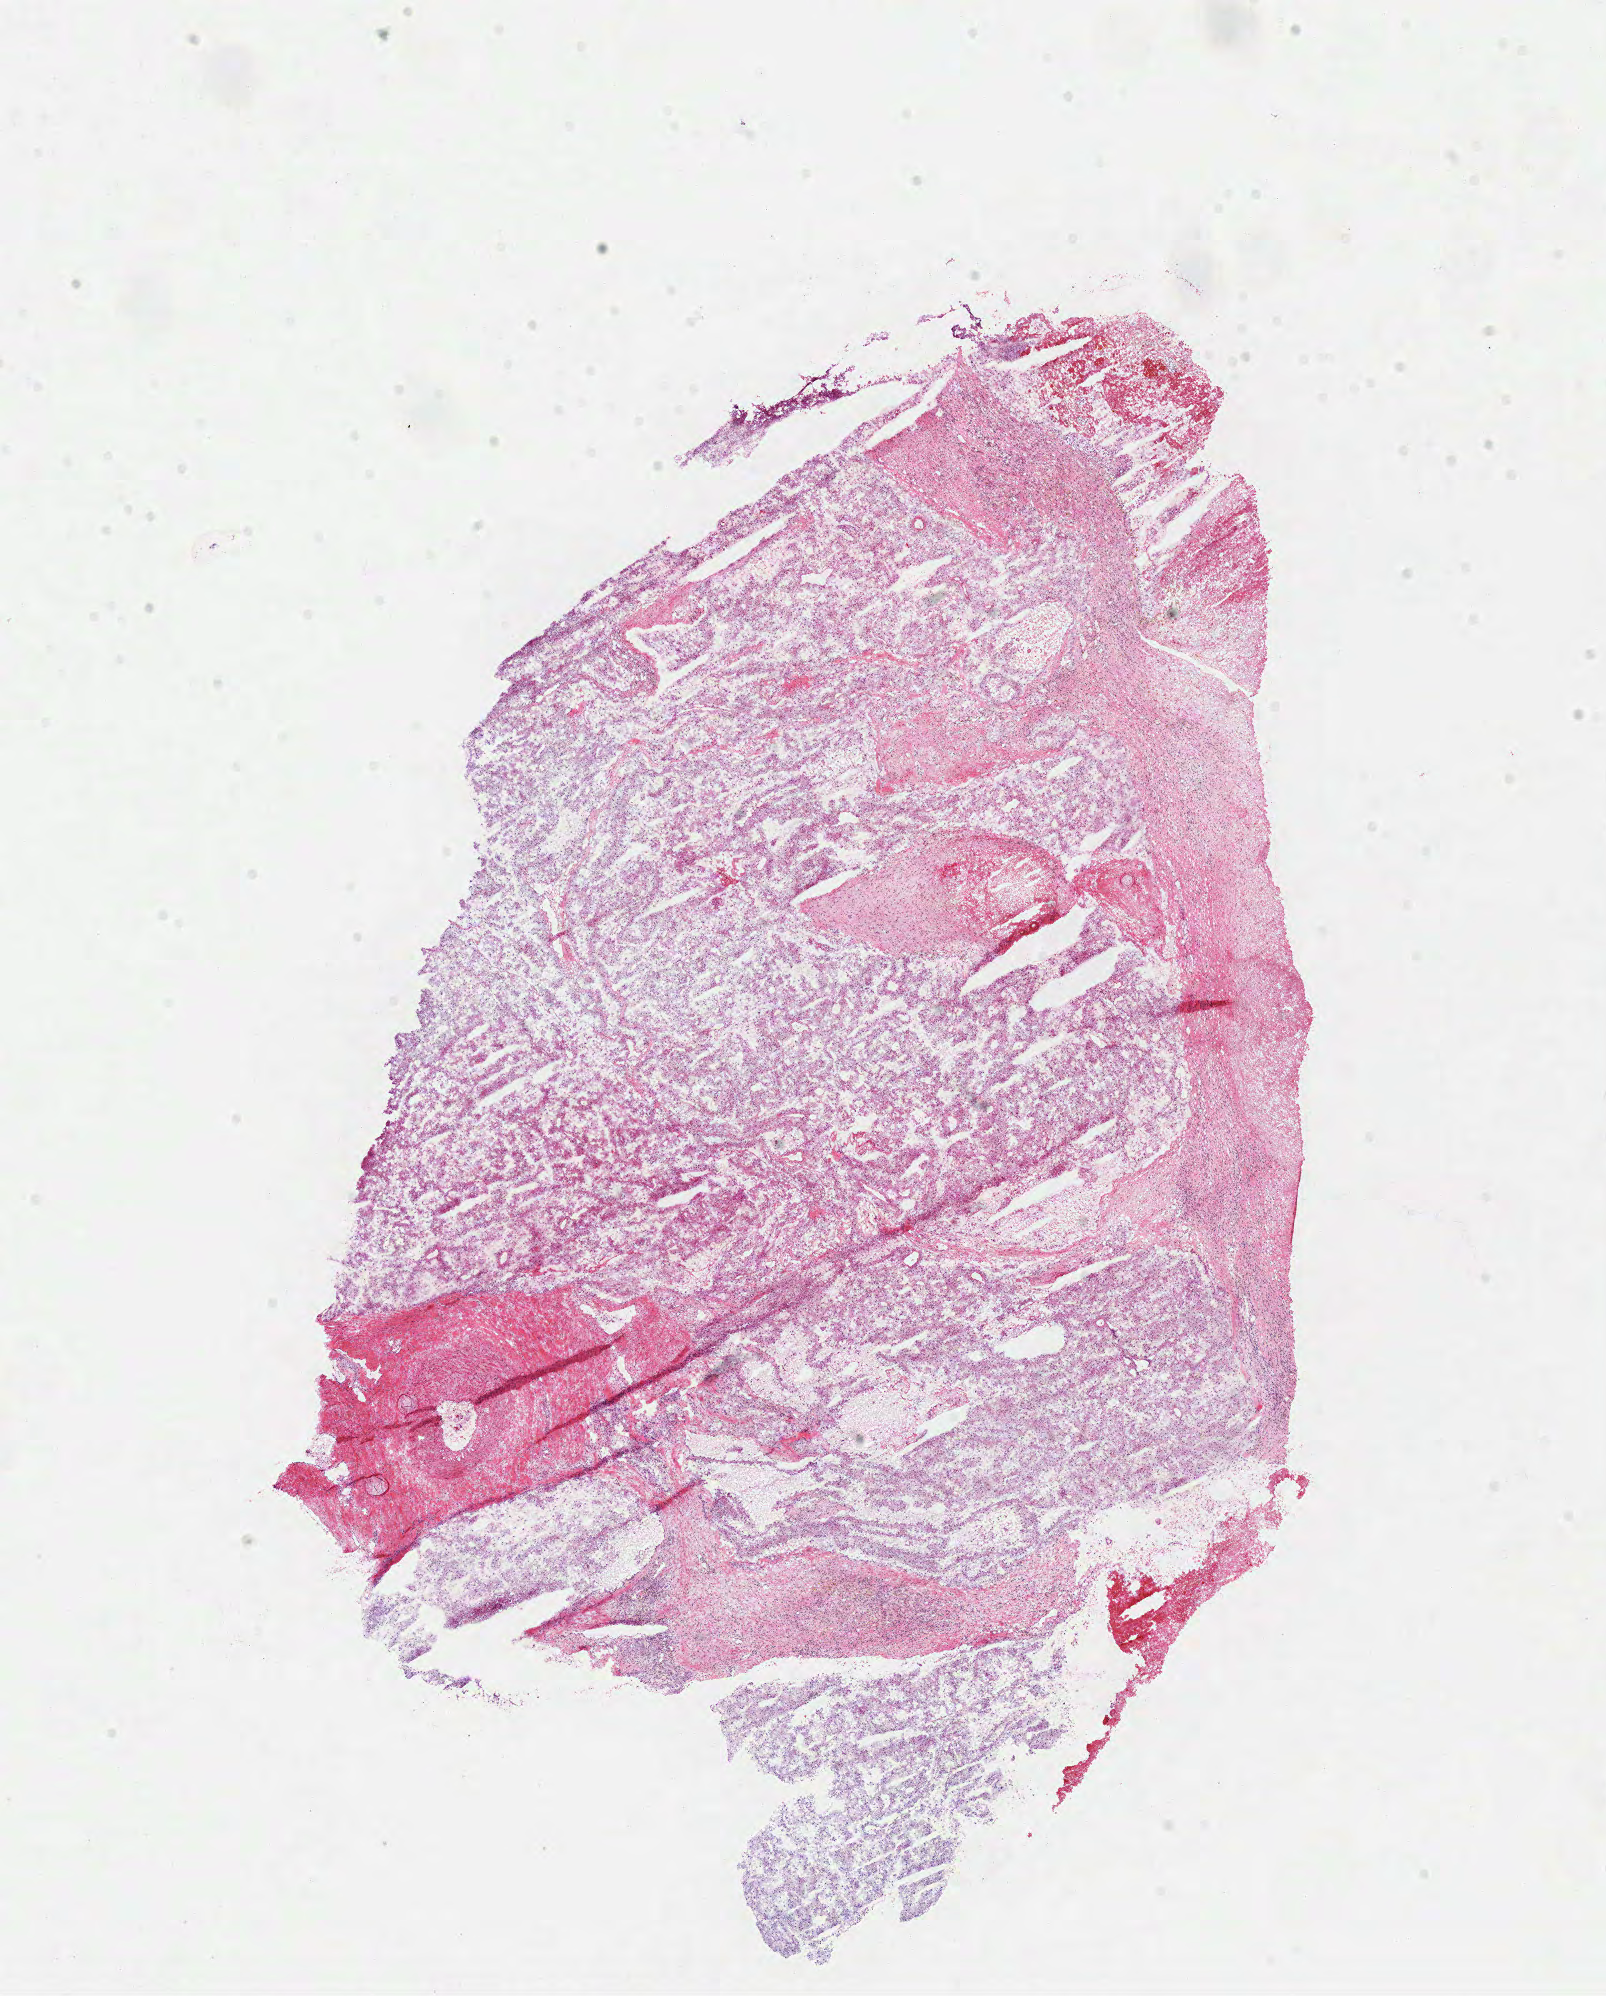
Digitized H&E-stained tissue section (whole slide), shown as a low-resolution overview of the whole scanned area (about 12.7 x 15.7 mm, acquisition: 40x scan); frozen section; primary tumour sample from the kidney. Male patient; age at initial diagnosis 54 years. Slide review estimates, as recorded: tumour cells 85%, tumour nuclei 80%.
Diagnosis: Papillary adenocarcinoma, NOS.